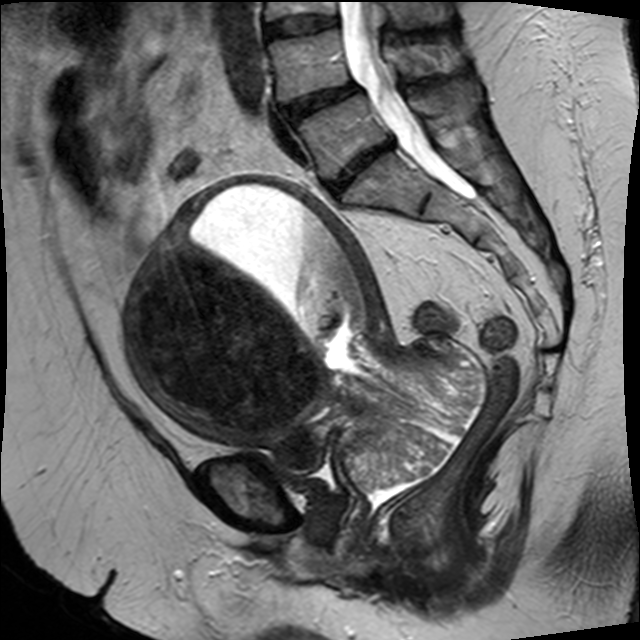
Pelvic MRI for cervical cancer, one sagittal slice; position 18 of 34 along the scan axis; T2-weighted; 1.5 T; TE 89 ms, TR 3320 ms; 640 × 640 image matrix, field of view 260 × 260 mm. Female patient, age 50 years.
Outlined on this slice (manually delineated by an expert):
- uterus and cervix: bounding box <128,172,486,493> (left, top, right, bottom; pixels)